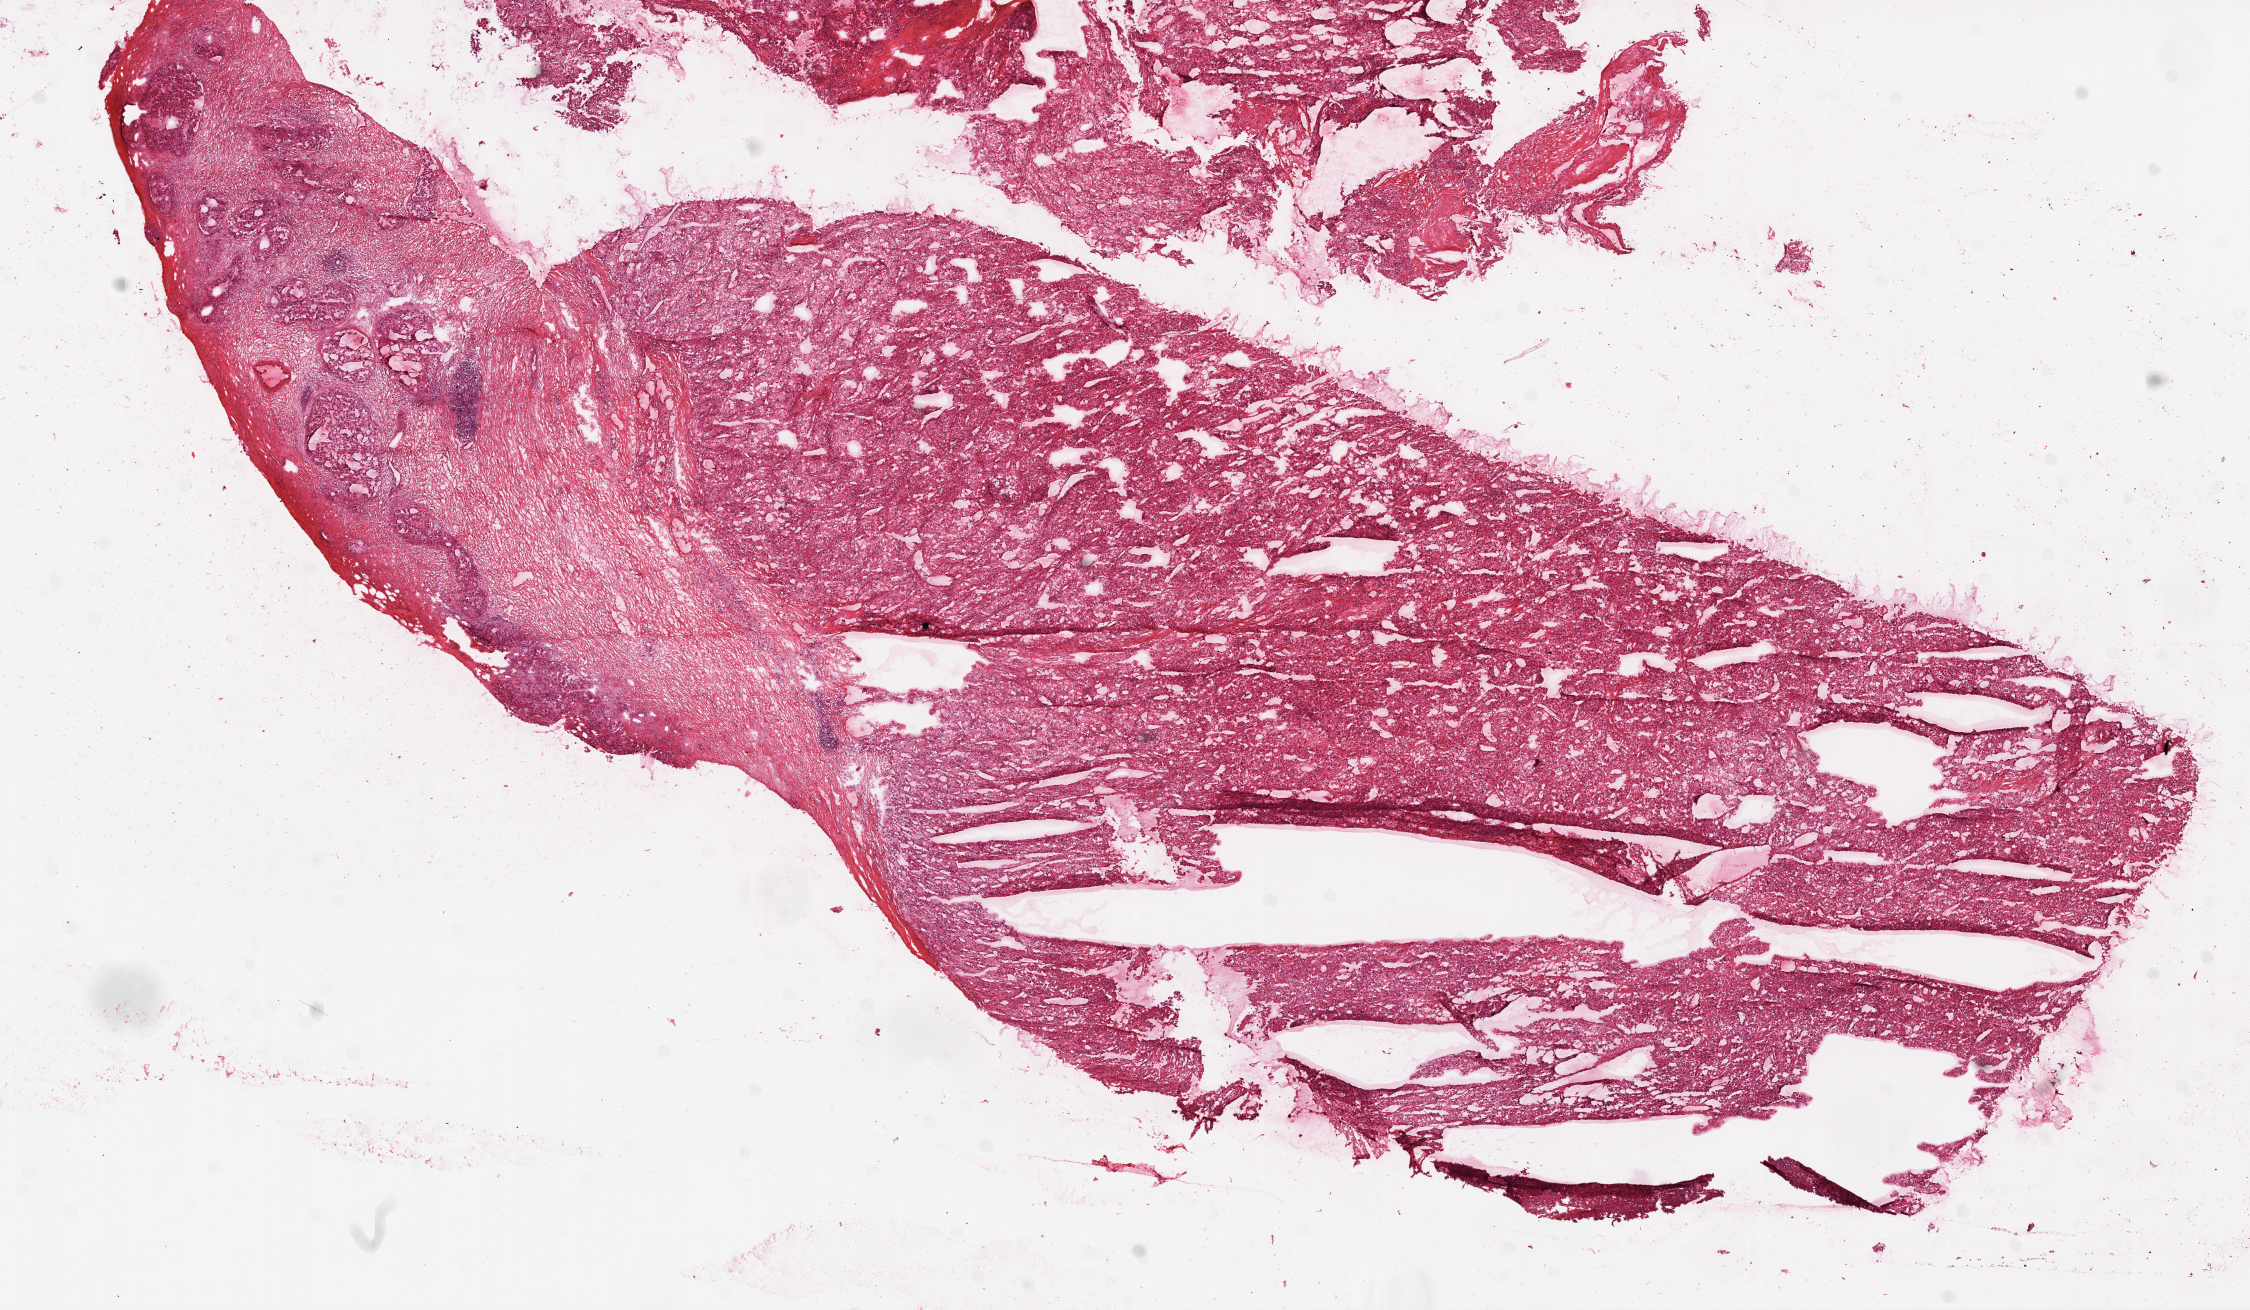
Digitized H&E-stained tissue section (whole slide) — low-resolution overview of the scanned area, about 18.1 x 10.5 mm (slide scanned at 20x); frozen section from the top of the tissue portion; kidney, primary tumour sample. Patient: male, age at initial diagnosis 60 years. Histologic grade: G3 (poorly differentiated). Pathologist review of this section (percent, as recorded): tumour cells 70%, tumour nuclei 85%, normal cells 0%, stromal cells 30%, necrosis 0%.
* AJCC pathologic stage: IV
* TNM: T3a NX M1
* histologic diagnosis: Clear cell adenocarcinoma, NOS